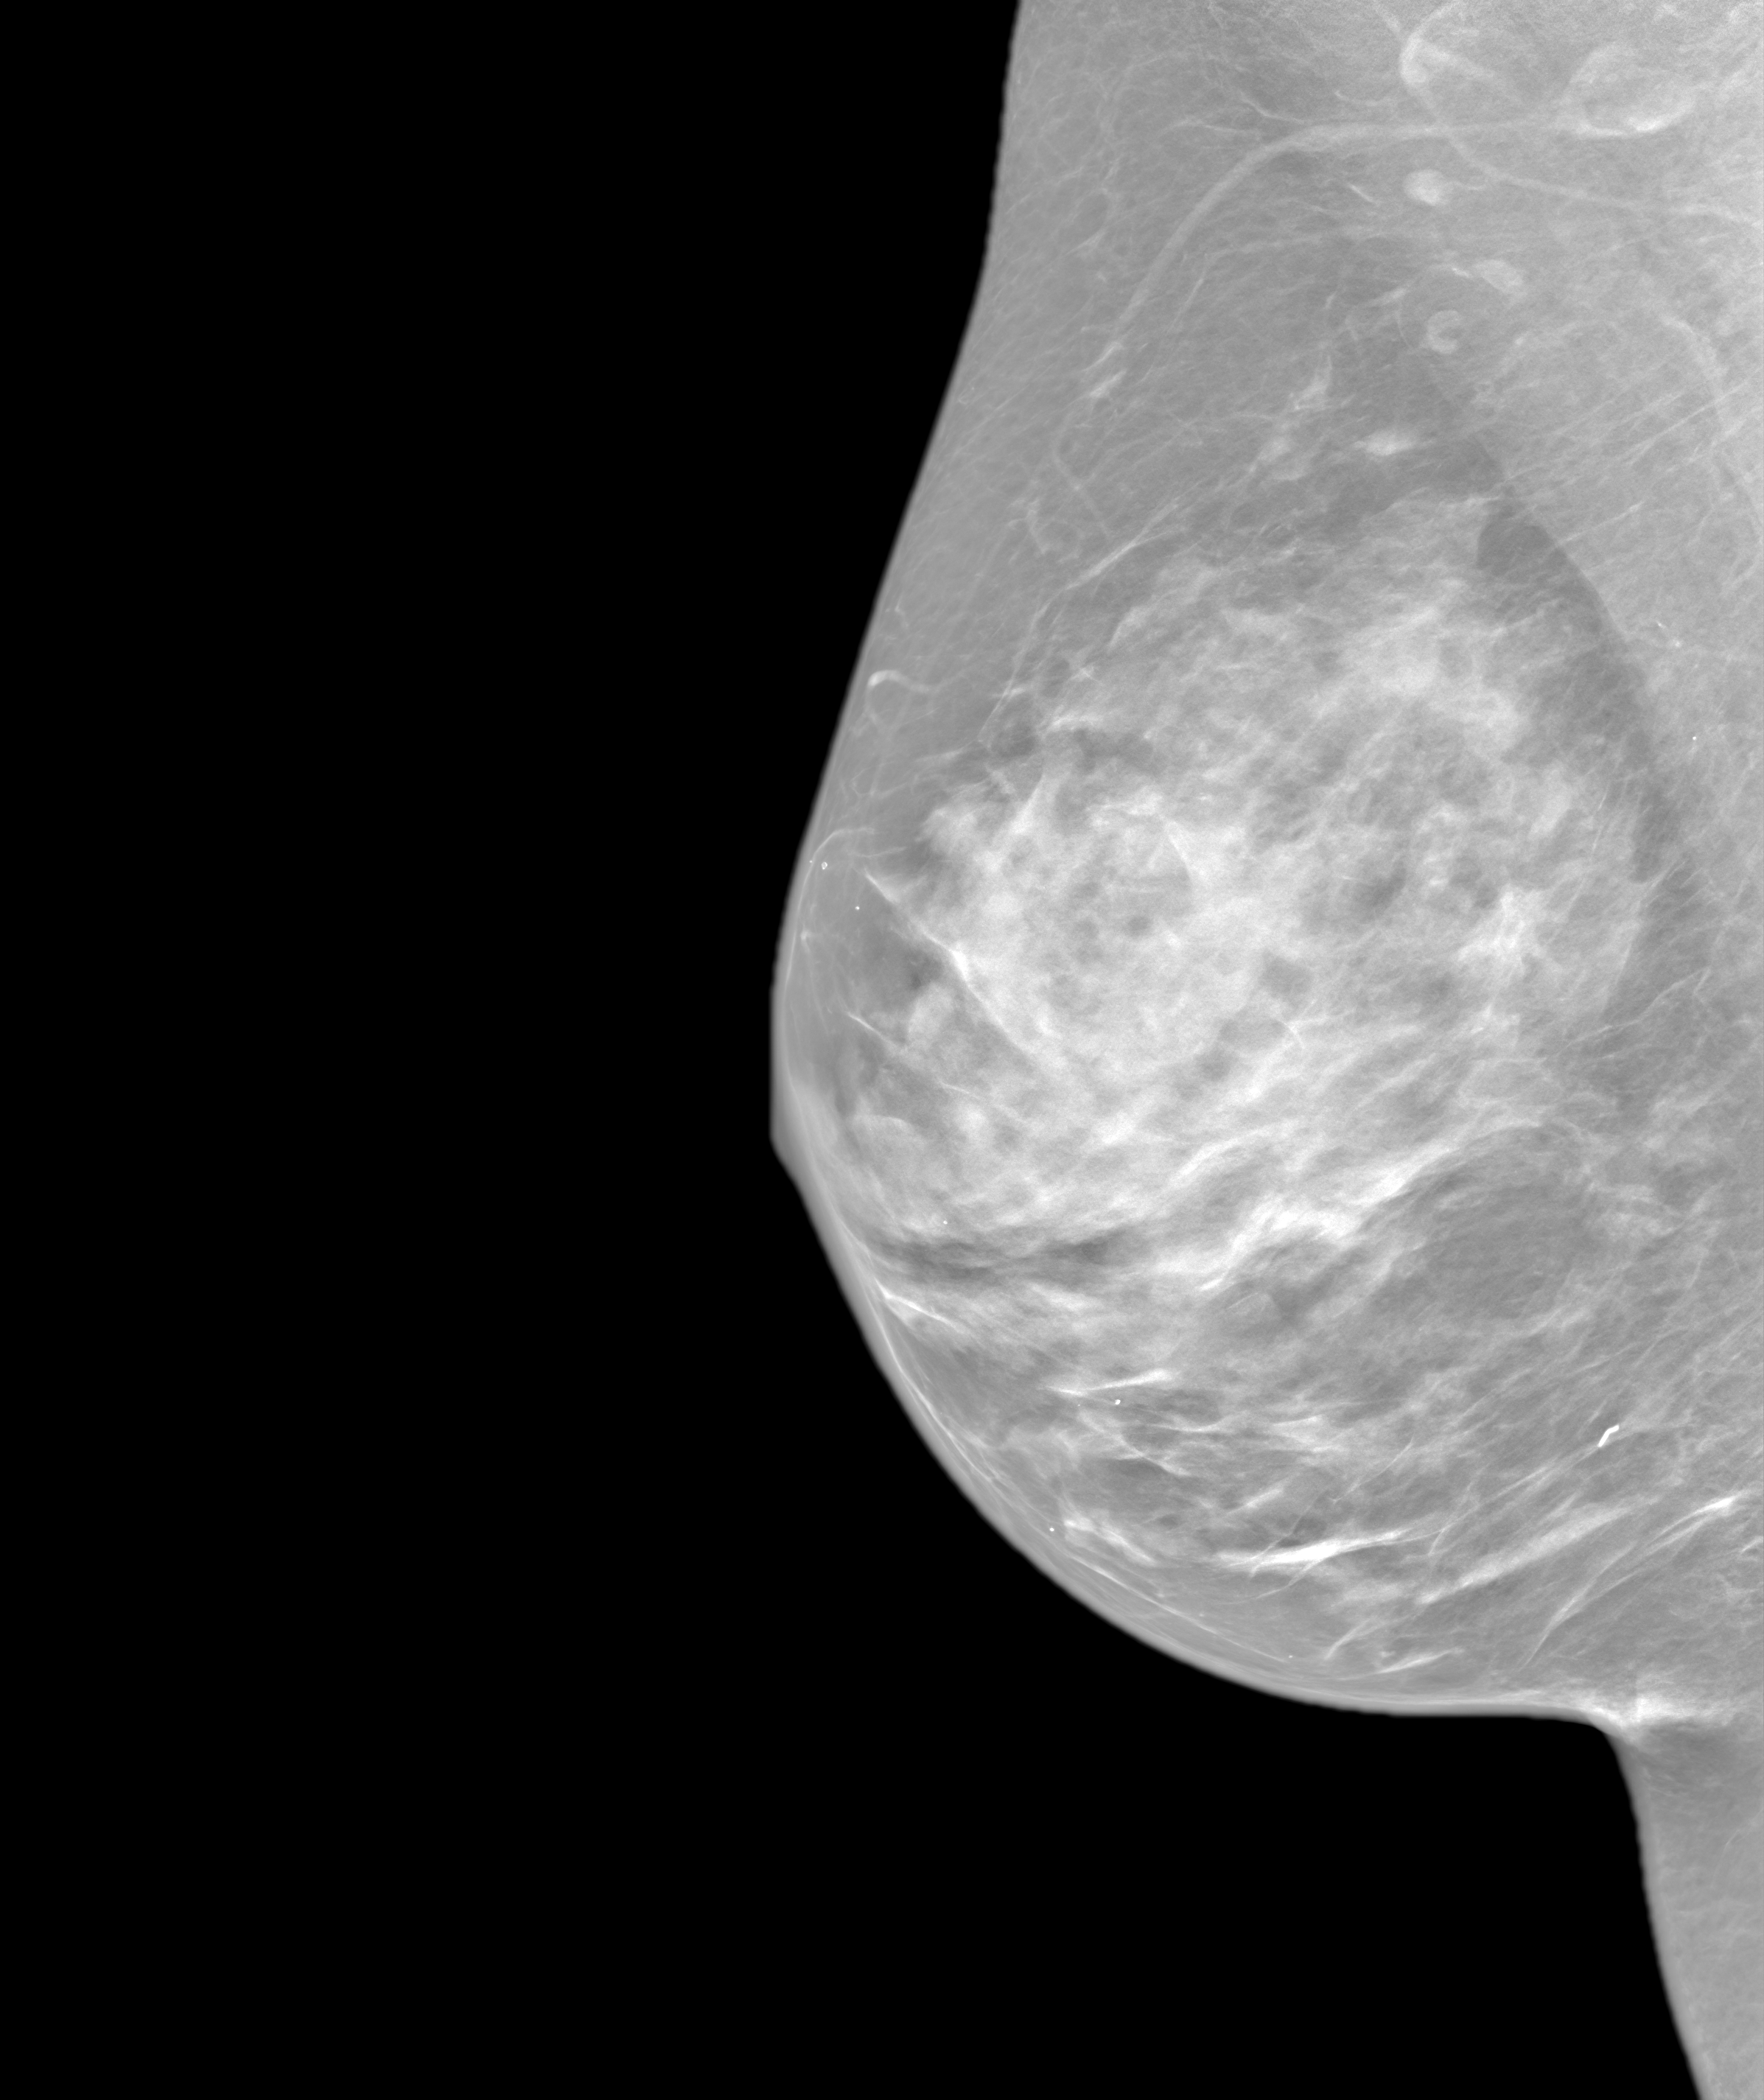
Annual screening mammography examination; system: SenoIris_1SP1.2(425). Patient: female, 65 years.
Image type: synthesized 2-D view from tomosynthesis. Breast: right. Projection: MLO view.